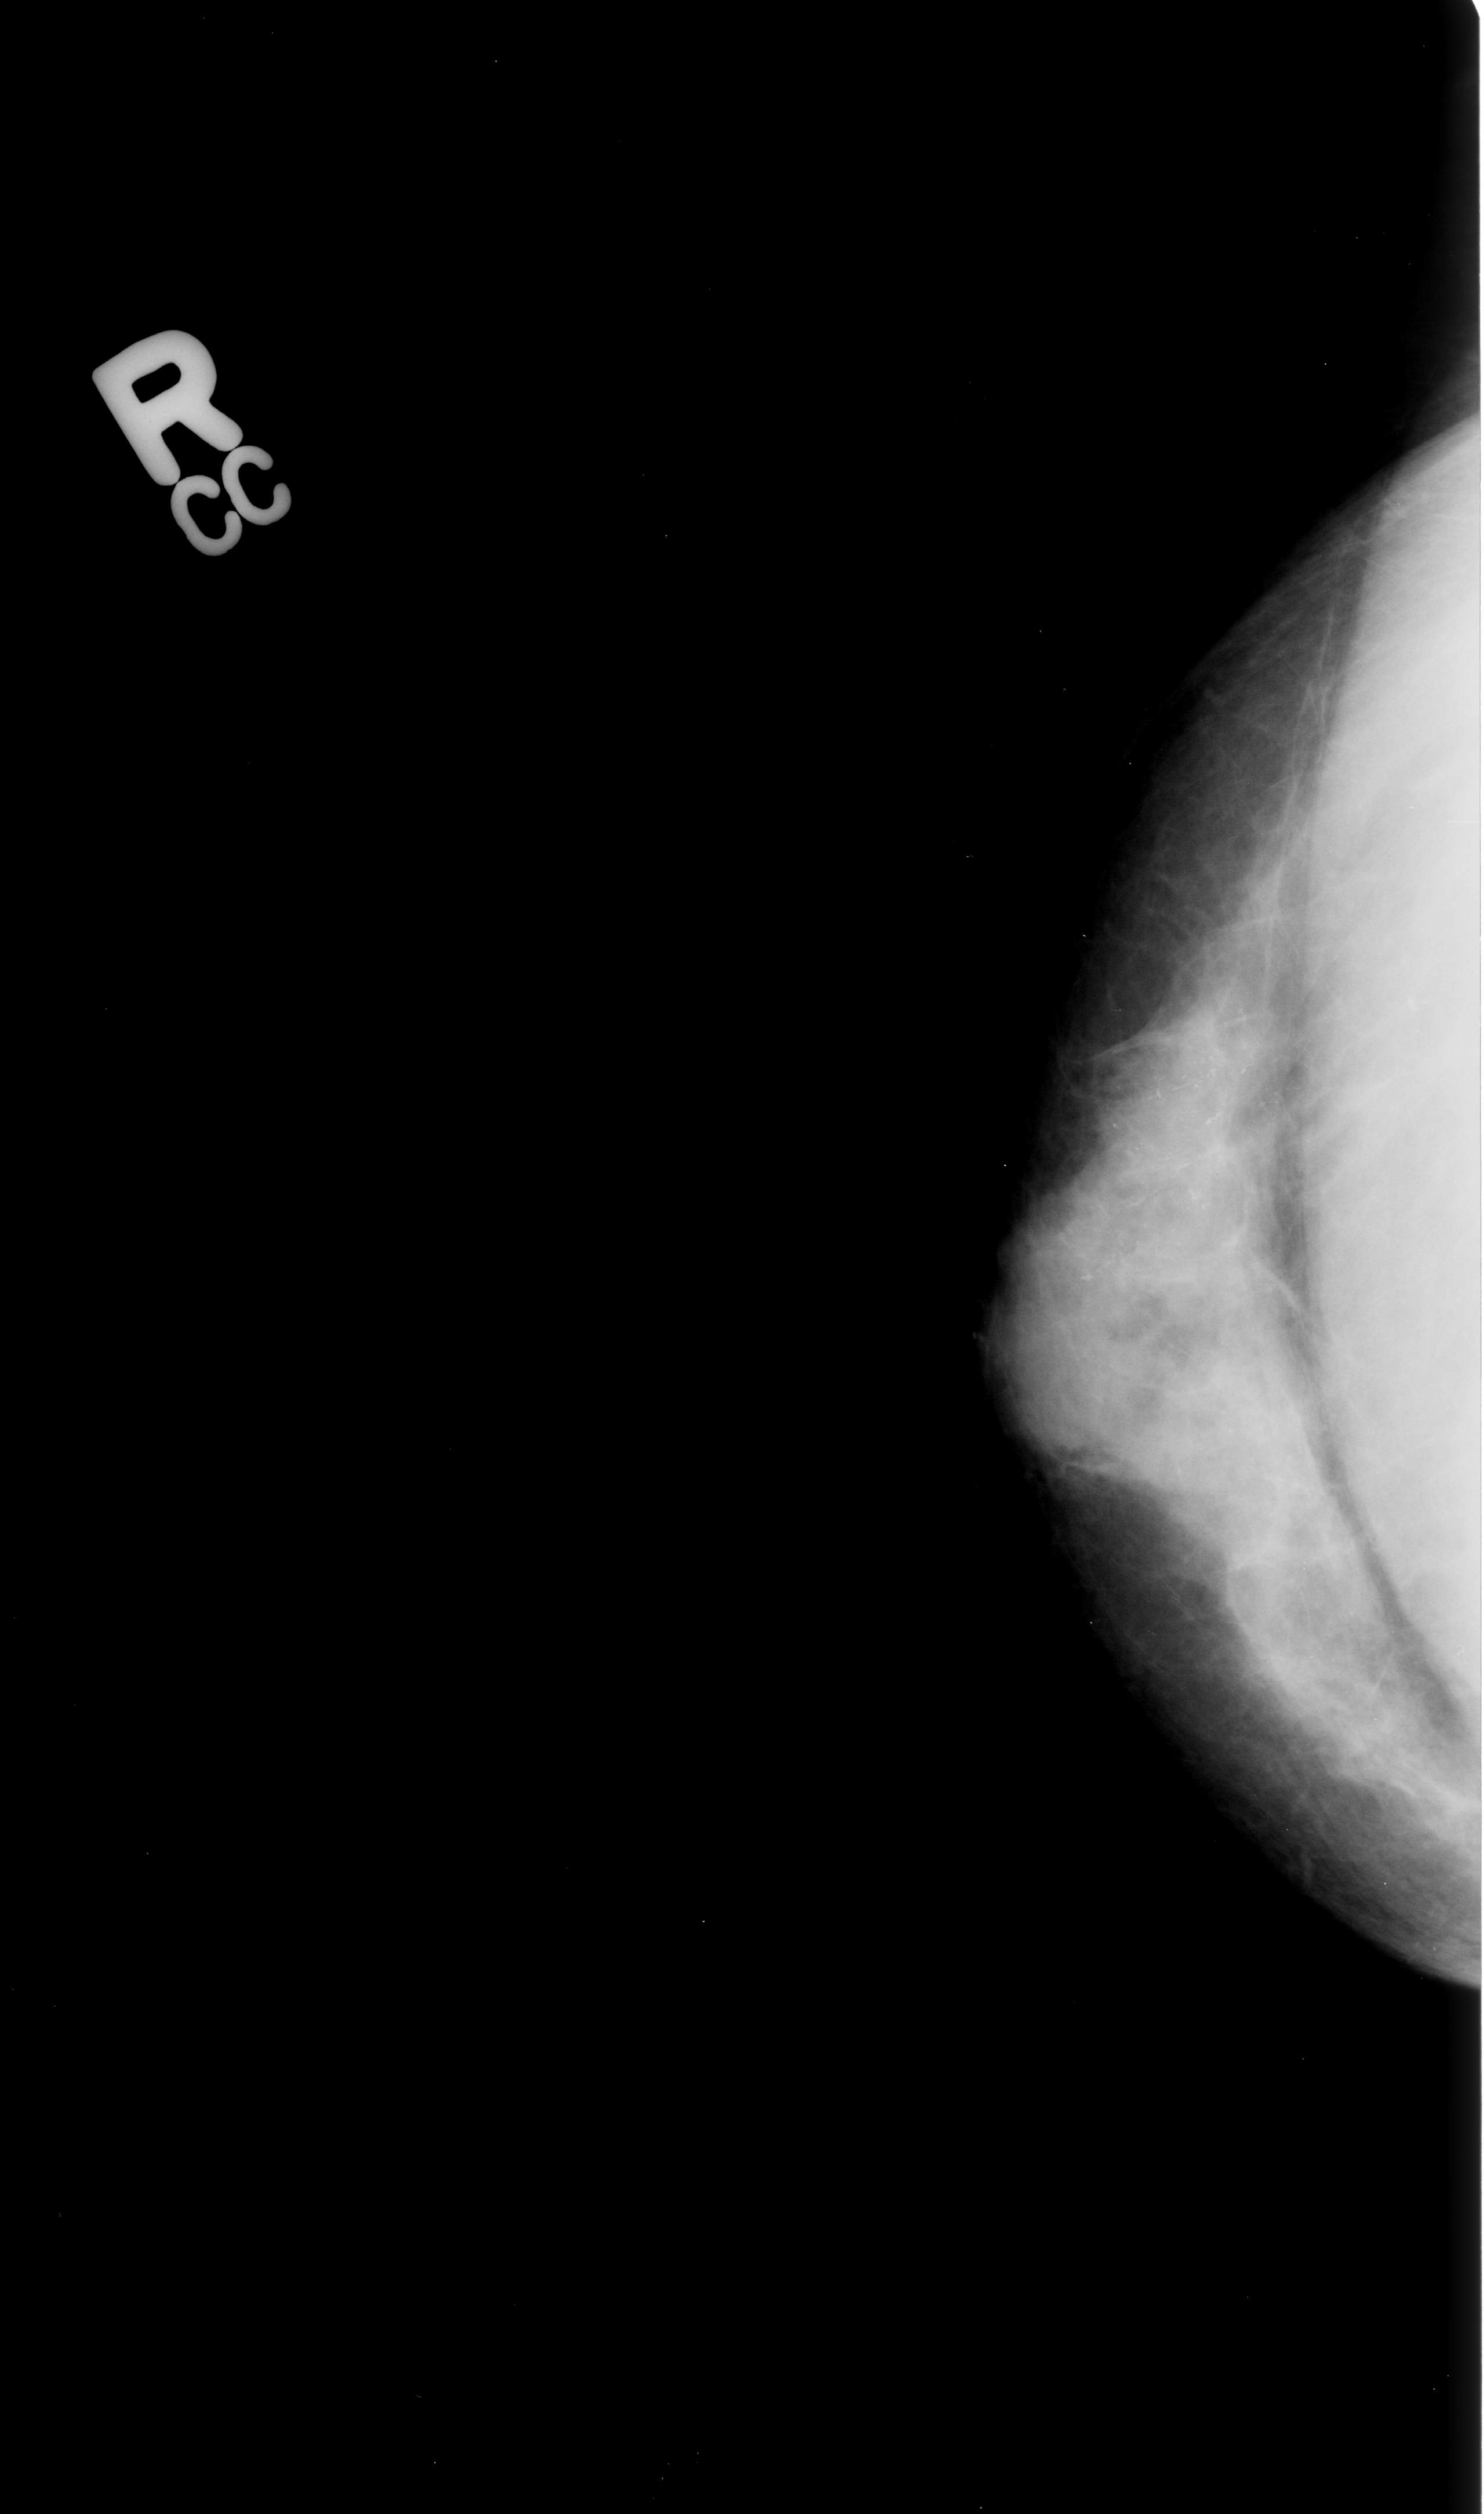
Digitized screen-film mammogram, right breast, CC view, BI-RADS breast density category 3 (scale 1–4).
Finding: calcifications, morphology fine linear branching, distribution linear / segmental; BI-RADS assessment category 5; pathology (as recorded): malignant.